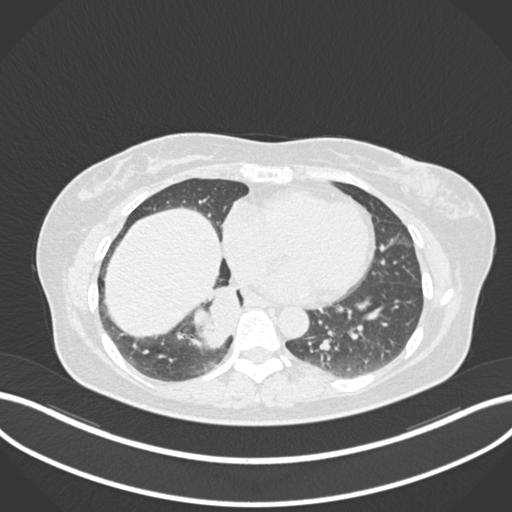
Chest CT, one axial slice; position 552 of 677 along the scan axis; reconstruction kernel B30f; 120 kVp; lung window (W 1500 / L -600 HU); 512 × 512 image matrix, field of view 400 × 400 mm. Female patient, age 54 years. Case-level facts recorded for this patient, not image findings: clinical TNM (as recorded): T4 N0 M0.
Annotated regions visible in this slice (rectangle marked by the reading radiologist):
- lung tumour (recorded histology: adenocarcinoma): bounding box [x1, y1, x2, y2] px = [190, 275, 244, 357]